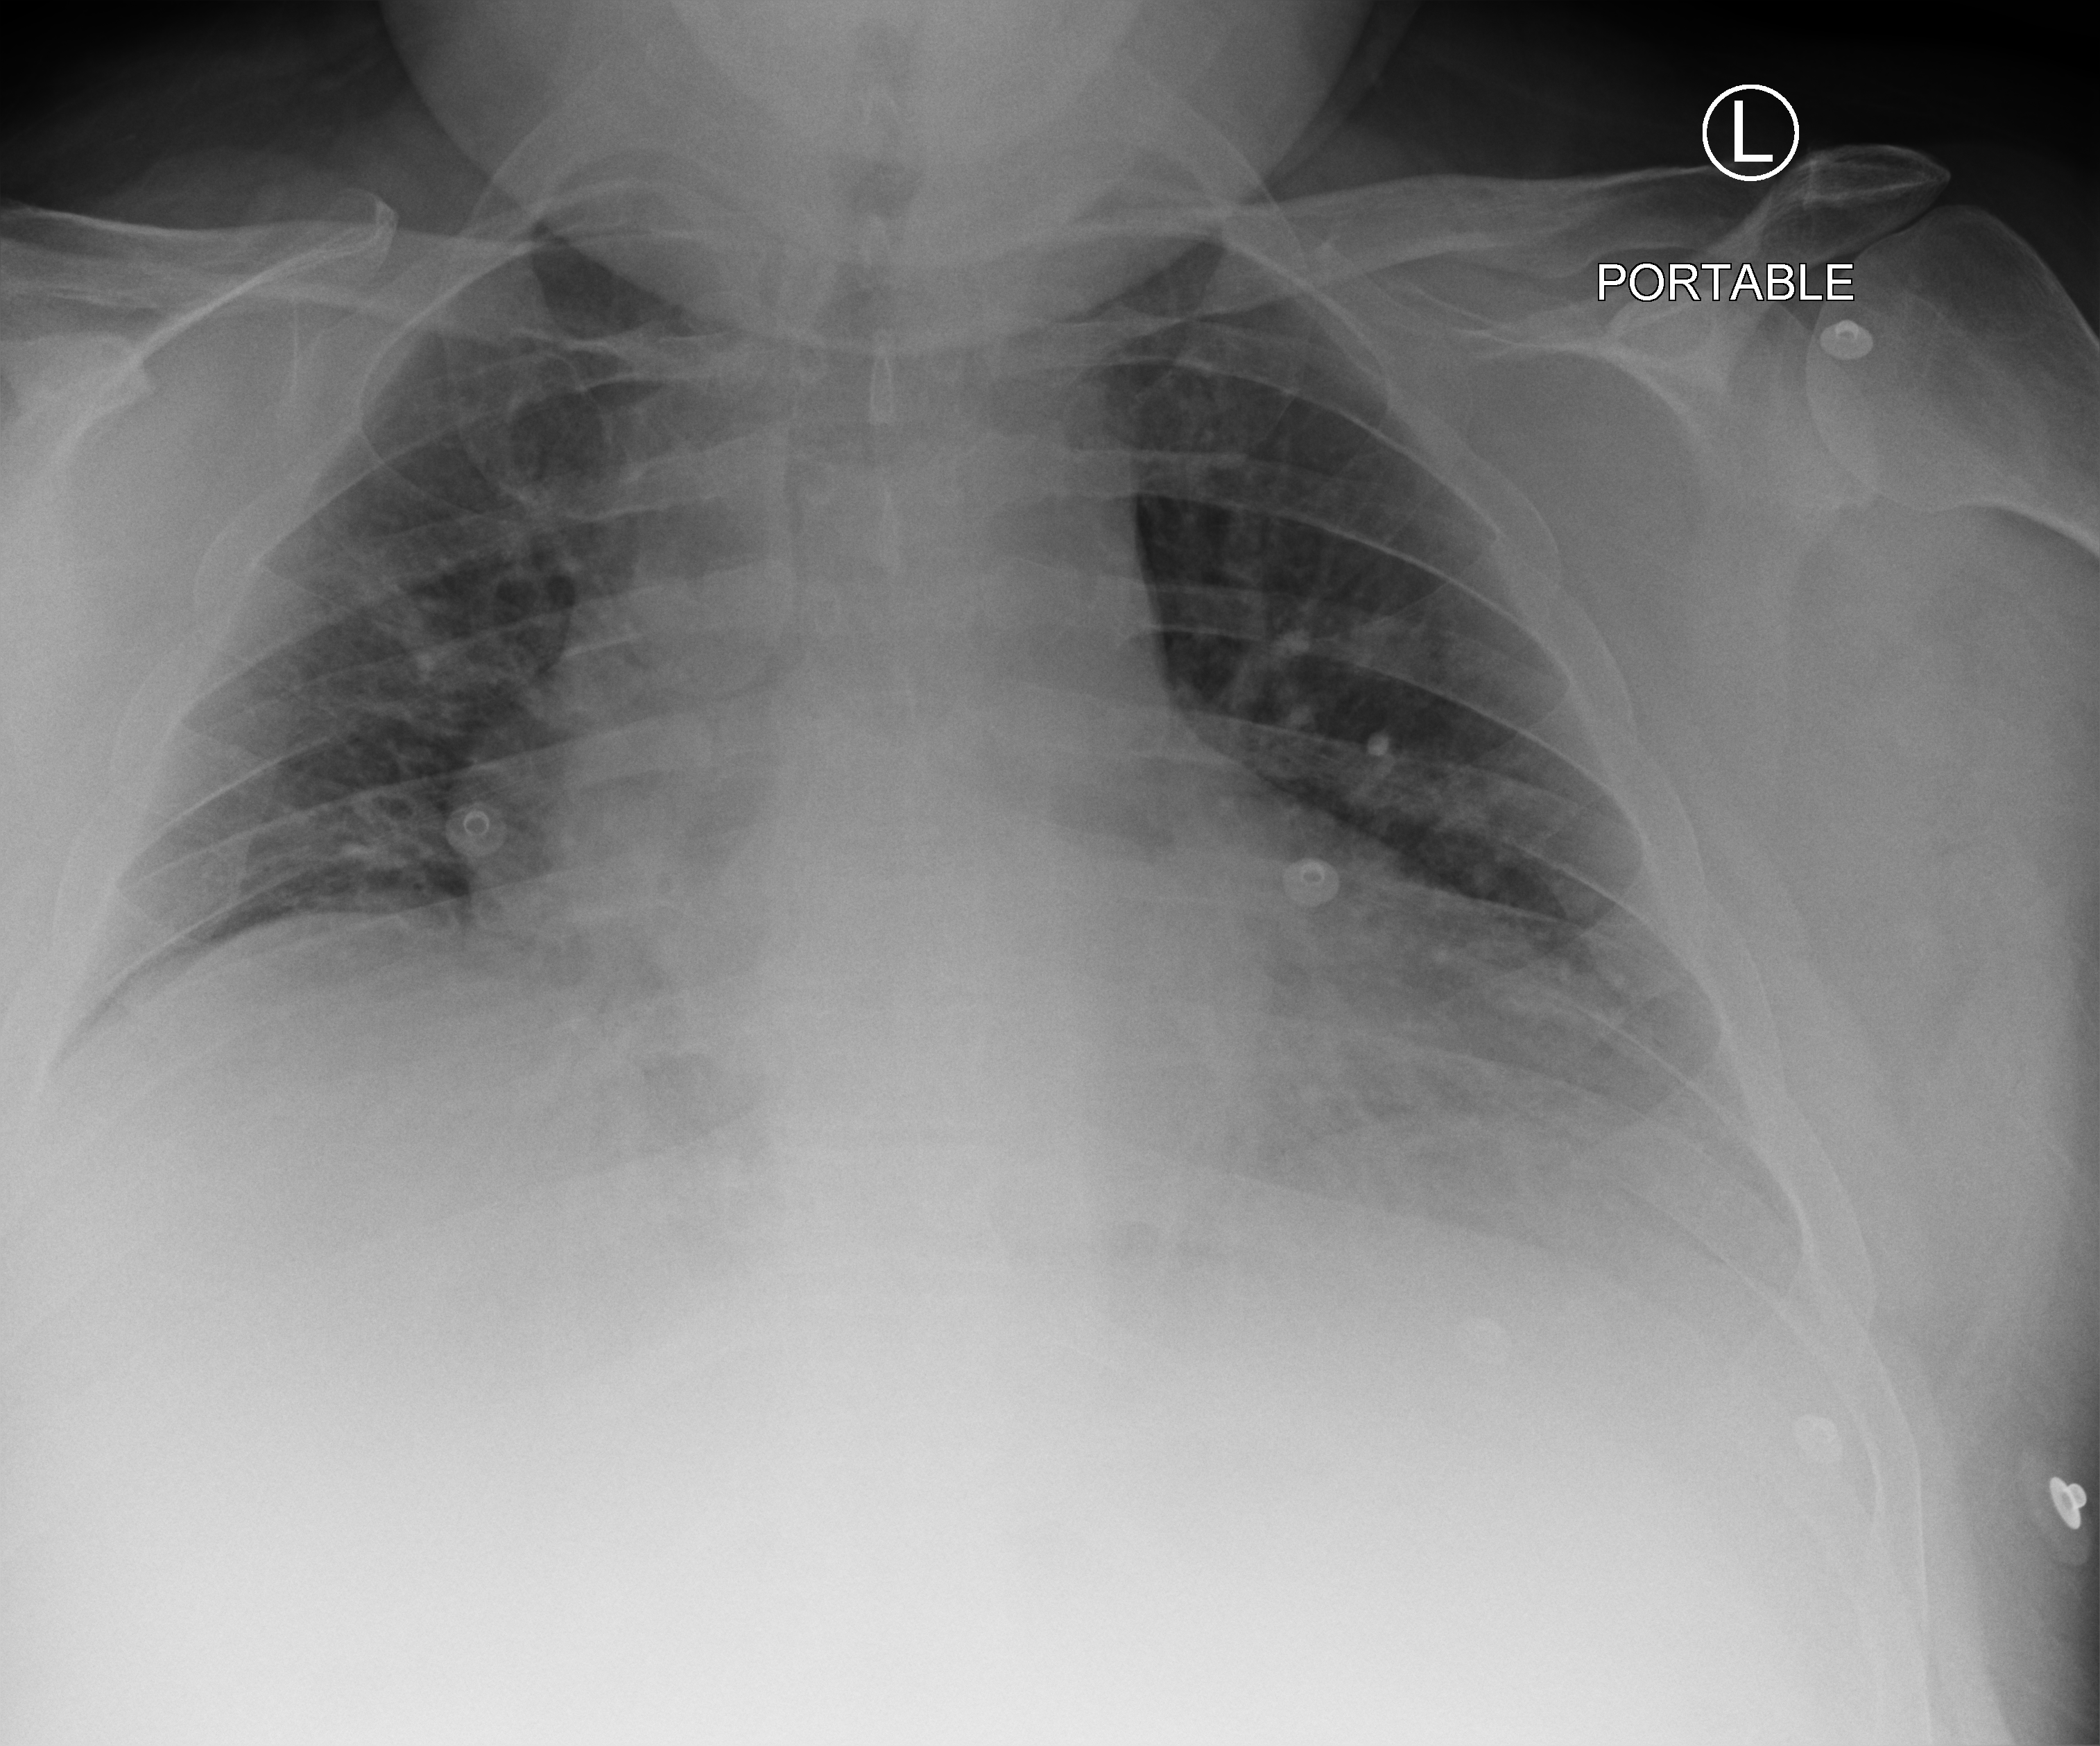
Portable chest radiograph, anteroposterior (AP) projection. Patient hospitalised with COVID-19; male, aged 18–59 years.
Hospital-stay facts (about this admission, not read from this image; timing relative to this image not recorded): admitted to intensive care during this hospital stay: no; mechanically ventilated during this hospital stay: no.